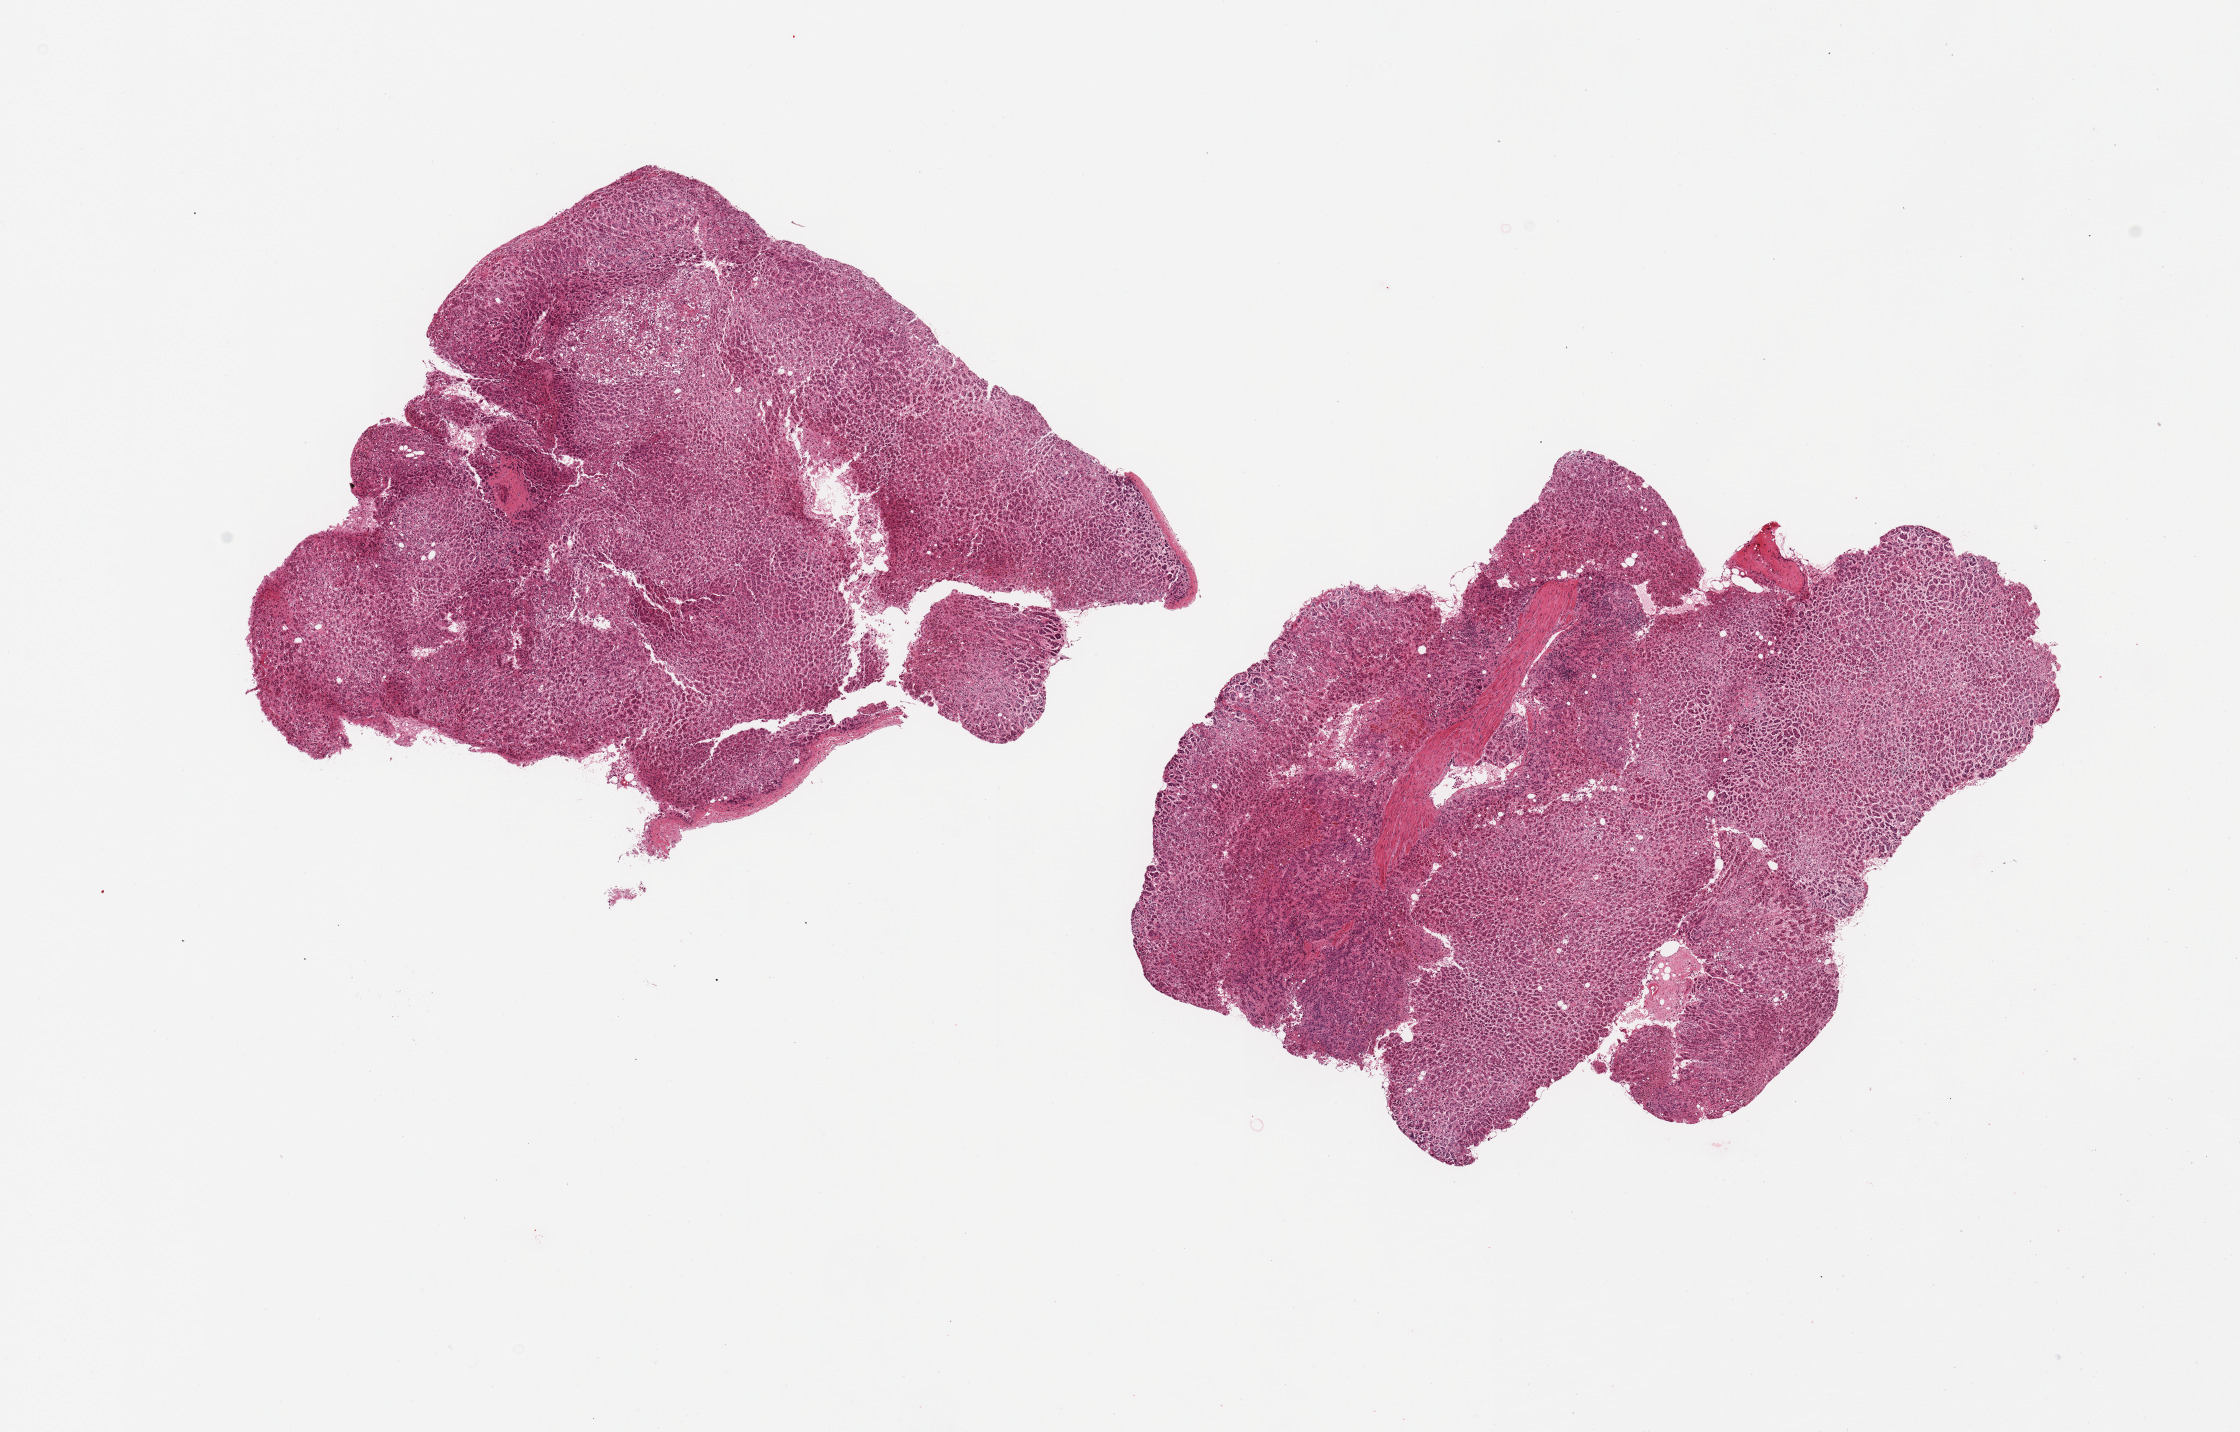
Whole-slide image, hematoxylin and eosin (H&E) stain, brightfield — low-resolution overview of the scanned area, about 17.7 x 11.3 mm; PAXgene-fixed, paraffin-embedded tissue; section of adrenal gland (target tissue); donor tissue sample.
Pathologist's review note for this sample: 2 pieces, all cortex.